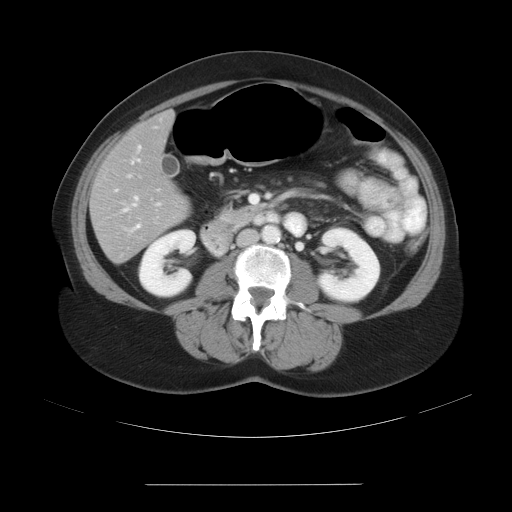
Contrast-enhanced abdominal CT, one axial slice; position 9 of 27 along the scan axis; reconstruction kernel STANDARD; soft-tissue window (W 400 / L 40 HU); 7.5 mm slice thickness; 512 × 512 image matrix, field of view 440 × 440 mm. Female patient, age 58 years. Case-level facts recorded for this patient, not image findings: diagnosis: colorectal cancer liver metastases, imaged before liver resection; multiple liver metastases: yes; largest metastasis: 1.9 cm; disease in both lobes: yes.
Structures marked on this image (expert manual segmentation):
- hepatic veins: box from (x=124, y=196) to (x=138, y=212) px
- liver: (x=92, y=113)–(x=188, y=263)
- planned liver remnant (the part of the liver to remain after resection): (x=96, y=113)–(x=175, y=197)
- portal vein (with intrahepatic branches): (x=115, y=144)–(x=161, y=231)